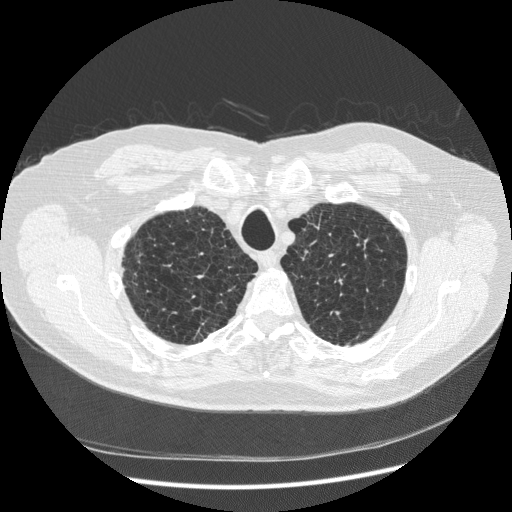
Chest CT (low-dose screening protocol), one axial image. Baseline annual screen. Lung window (W 1500 / L -600 HU). 1.25 mm slice thickness. Standard (soft-tissue) reconstruction kernel (STANDARD). 120 kVp. Slice 45 of 265 in the series. 512 × 512 image matrix. Male participant, aged 70 years at enrolment. Former smoker at enrolment.
Lesion marked by an expert reader, bounding box [x1, y1, x2, y2] px = [331, 216, 385, 270]. The screening reader recorded 2 non-calcified nodules or masses ≥4 mm on this exam; which of them this box marks is not recorded. Official screen result: positive, change unspecified: nodule(s) >= 4 mm or enlarging nodule(s), mass(es), or other non-specific abnormalities suspicious for lung cancer. Later outcome: lung cancer diagnosed 816 days after this screen — squamous cell carcinoma, NOS, left upper lobe, moderately differentiated (G2), stage IA (AJCC 6th edition), 18 mm at pathology.